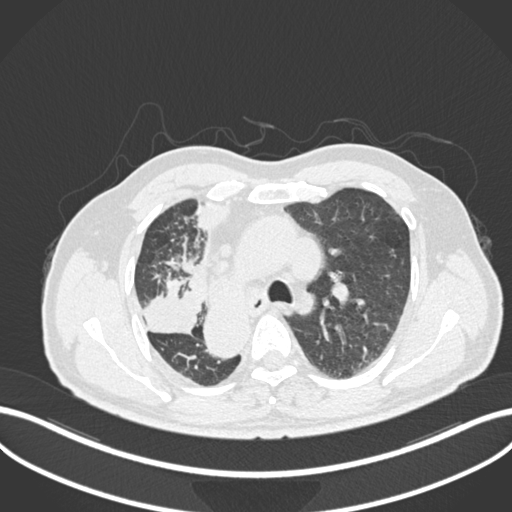
Chest CT, one axial slice. Position 165 of 206 along the scan axis. Reconstruction kernel B30f. 120 kVp. Lung window (W 1500 / L -600 HU). 512 × 512 image matrix, field of view 400 × 400 mm. Male patient, age 67 years. From the clinical record (not read from this slice): clinical TNM (as recorded): T2a N0 M0.
Outlined on this slice (rectangle marked by the reading radiologist):
- lung tumour (recorded histology: squamous cell carcinoma): bounding box (x1, y1, x2, y2) in pixels: (141, 283, 203, 340)